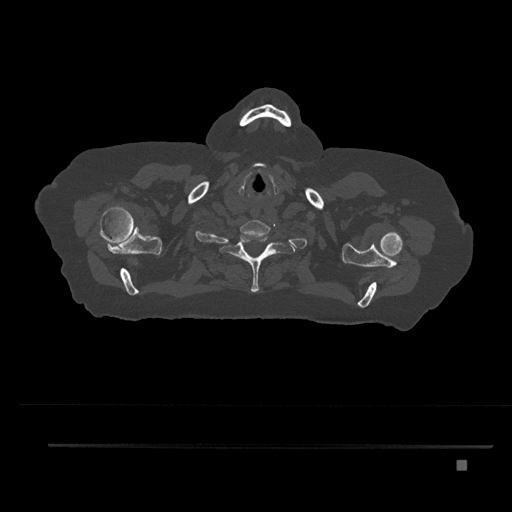
CT including the spine, one axial slice; reconstruction kernel Br40s/3; bone window (W 1800 / L 400 HU); 0.5 mm slice thickness; 512 × 512 image matrix, field of view 437 × 437 mm. Female patient, age 76 years. Case-level facts recorded for this patient, not image findings: primary cancer: lung.
Outlined on this slice (semi-automatic segmentation, software-assisted and operator-edited):
- T1 vertebra: bounding box <223,233,283,292> (left, top, right, bottom; pixels)